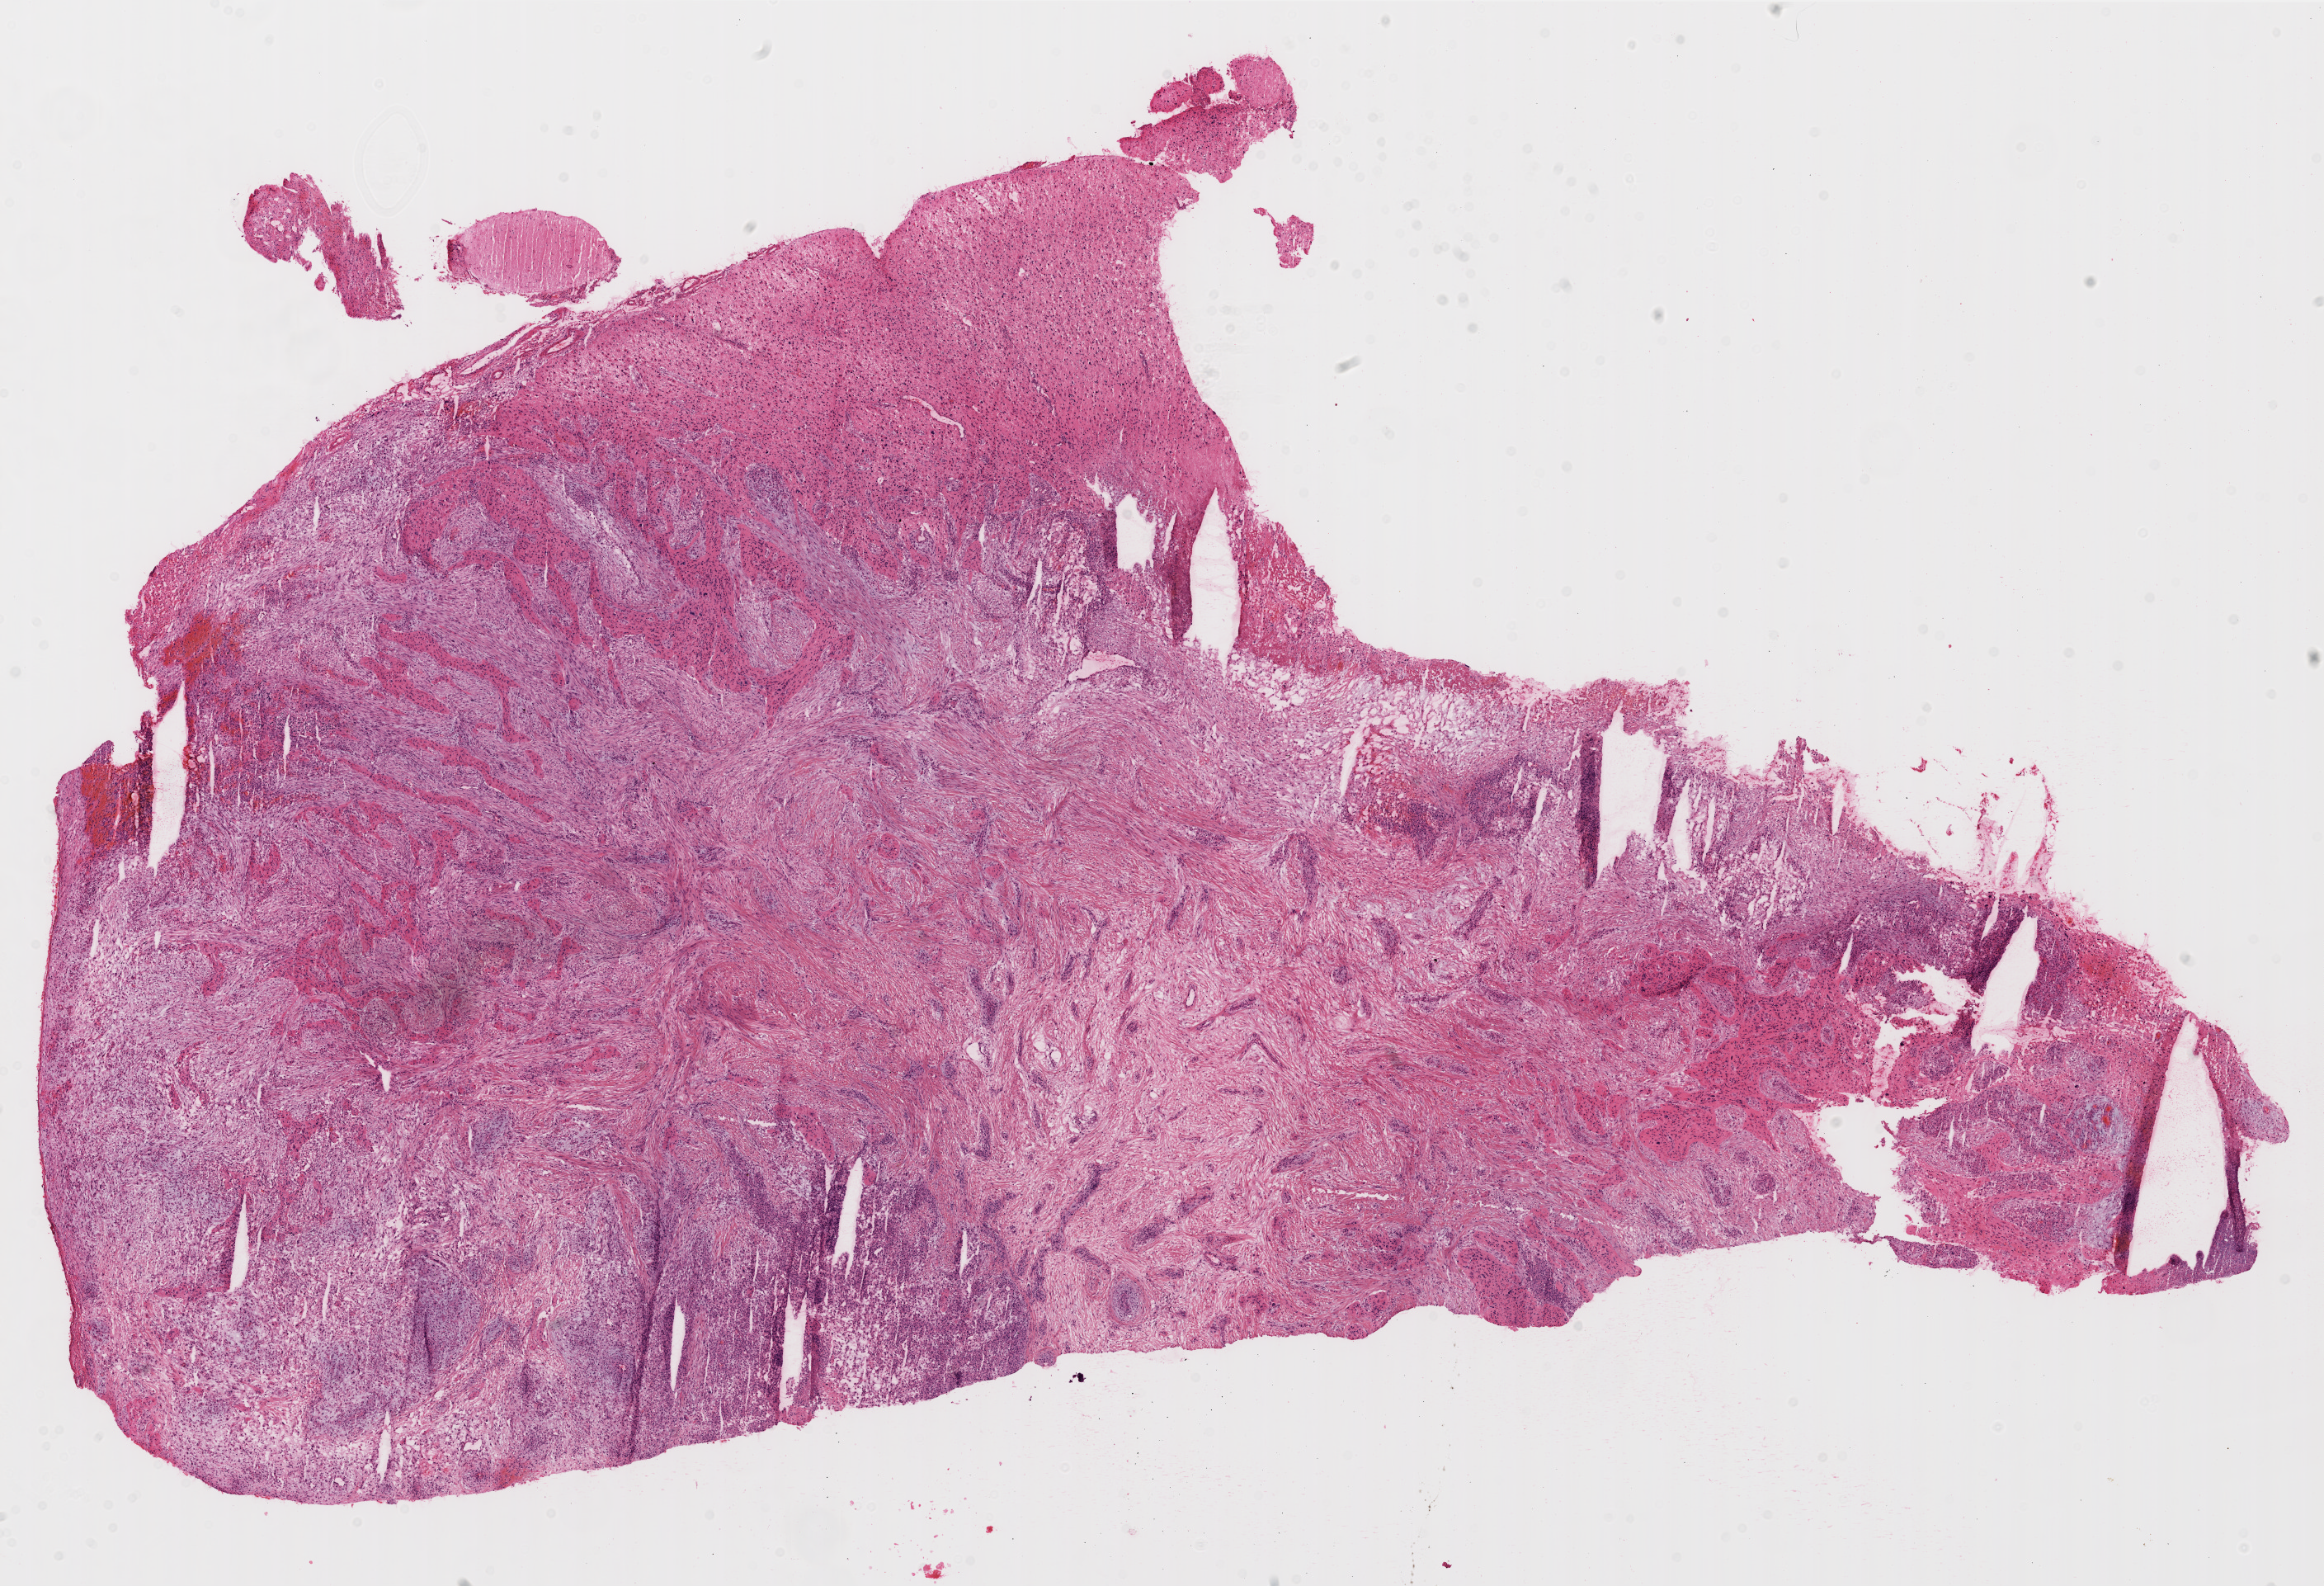
Whole-slide histology image, Hematoxylin and eosin (H&E) stained, shown as a low-resolution overview of the whole scanned area (about 22.7 x 15.5 mm, slide scanned at 20x). Formalin-fixed paraffin-embedded (FFPE) diagnostic section. Brain, primary tumour sample. Male, age 59 years at initial diagnosis.
Pathologic diagnosis: Glioblastoma.